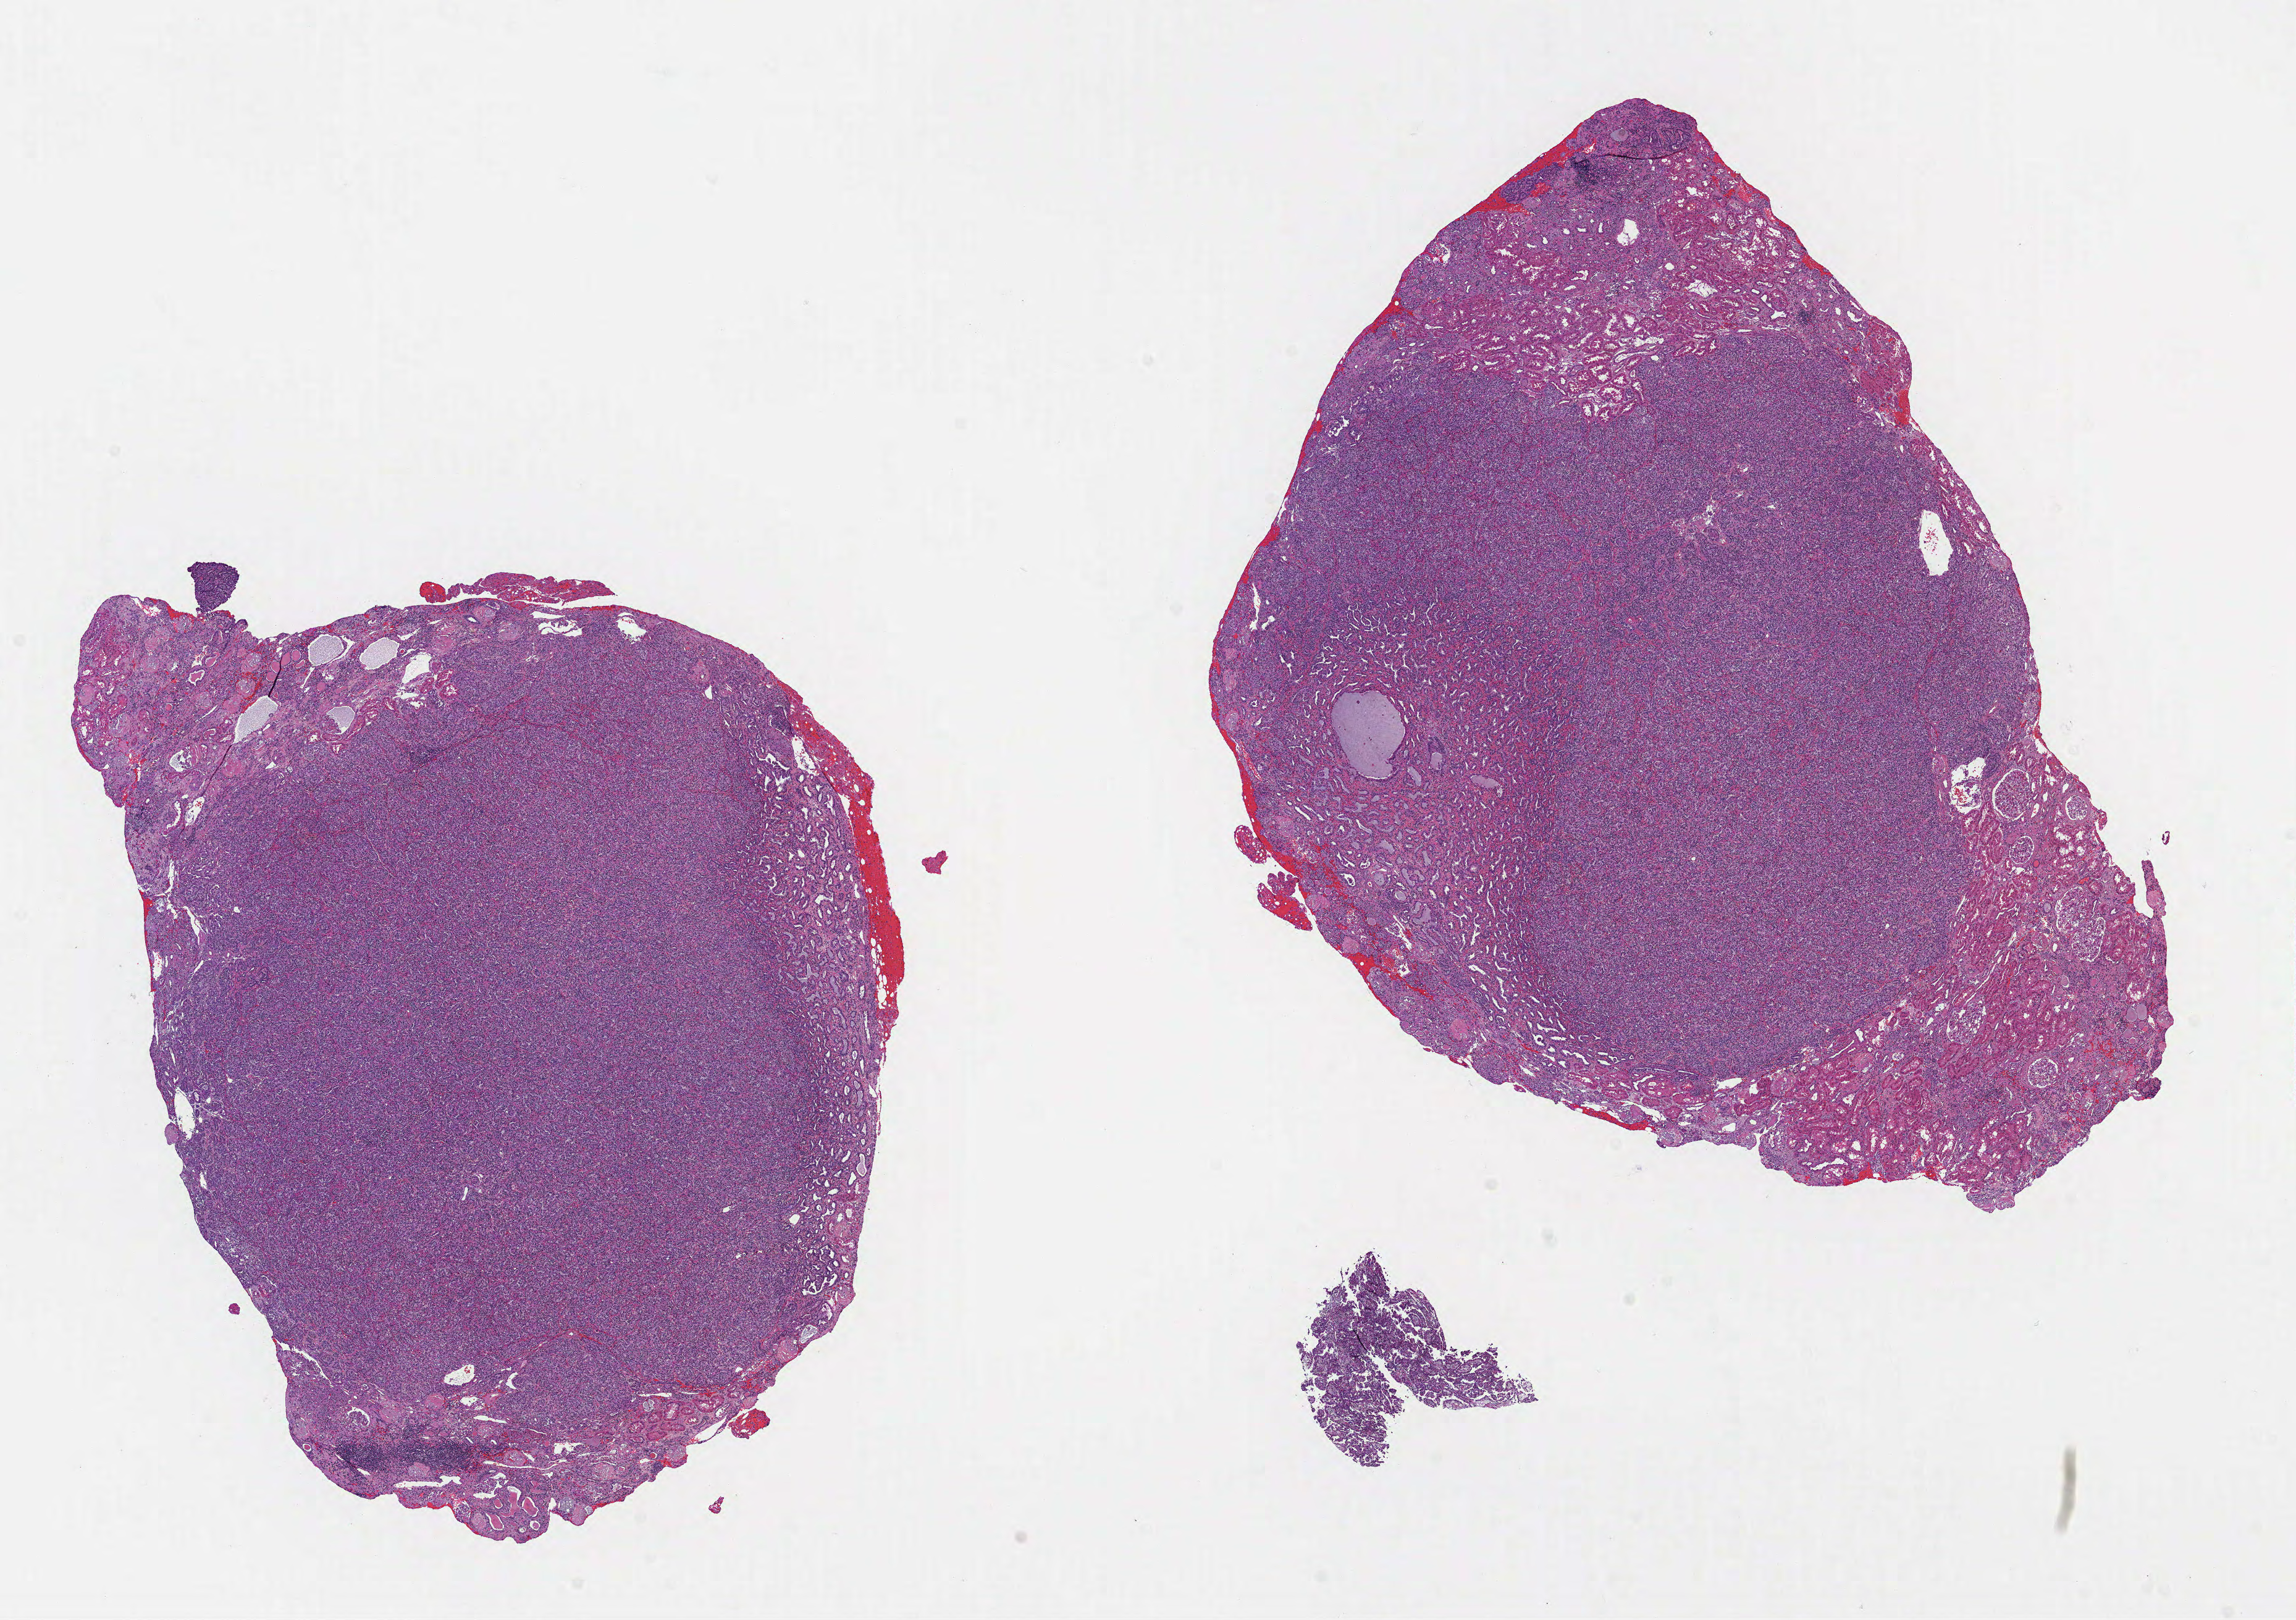
Digitized Hematoxylin and eosin (H&E) stained tissue section (whole slide), low-resolution overview of the scanned area, about 15.0 x 10.6 mm (slide scanned at 40x); formalin-fixed paraffin-embedded (FFPE) diagnostic section; sample: primary tumour, kidney. Patient: male, age at initial diagnosis 66 years.
Histologic diagnosis: Papillary adenocarcinoma, NOS. AJCC pathologic stage: I (6th edition). Laterality: left.